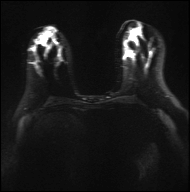
Breast MRI, one axial slice; position 16 of 36 along the scan axis; diffusion-weighted series; image 2 of 4 stored at this slice position (different b-values; order by instance number); 3 T; 4 mm slice thickness; 190 × 192 image matrix, field of view 317 × 320 mm. Female patient.
Structures marked on this image (manually delineated by an expert):
- tumour on diffusion-weighted imaging: box from (x=55, y=29) to (x=83, y=39) px